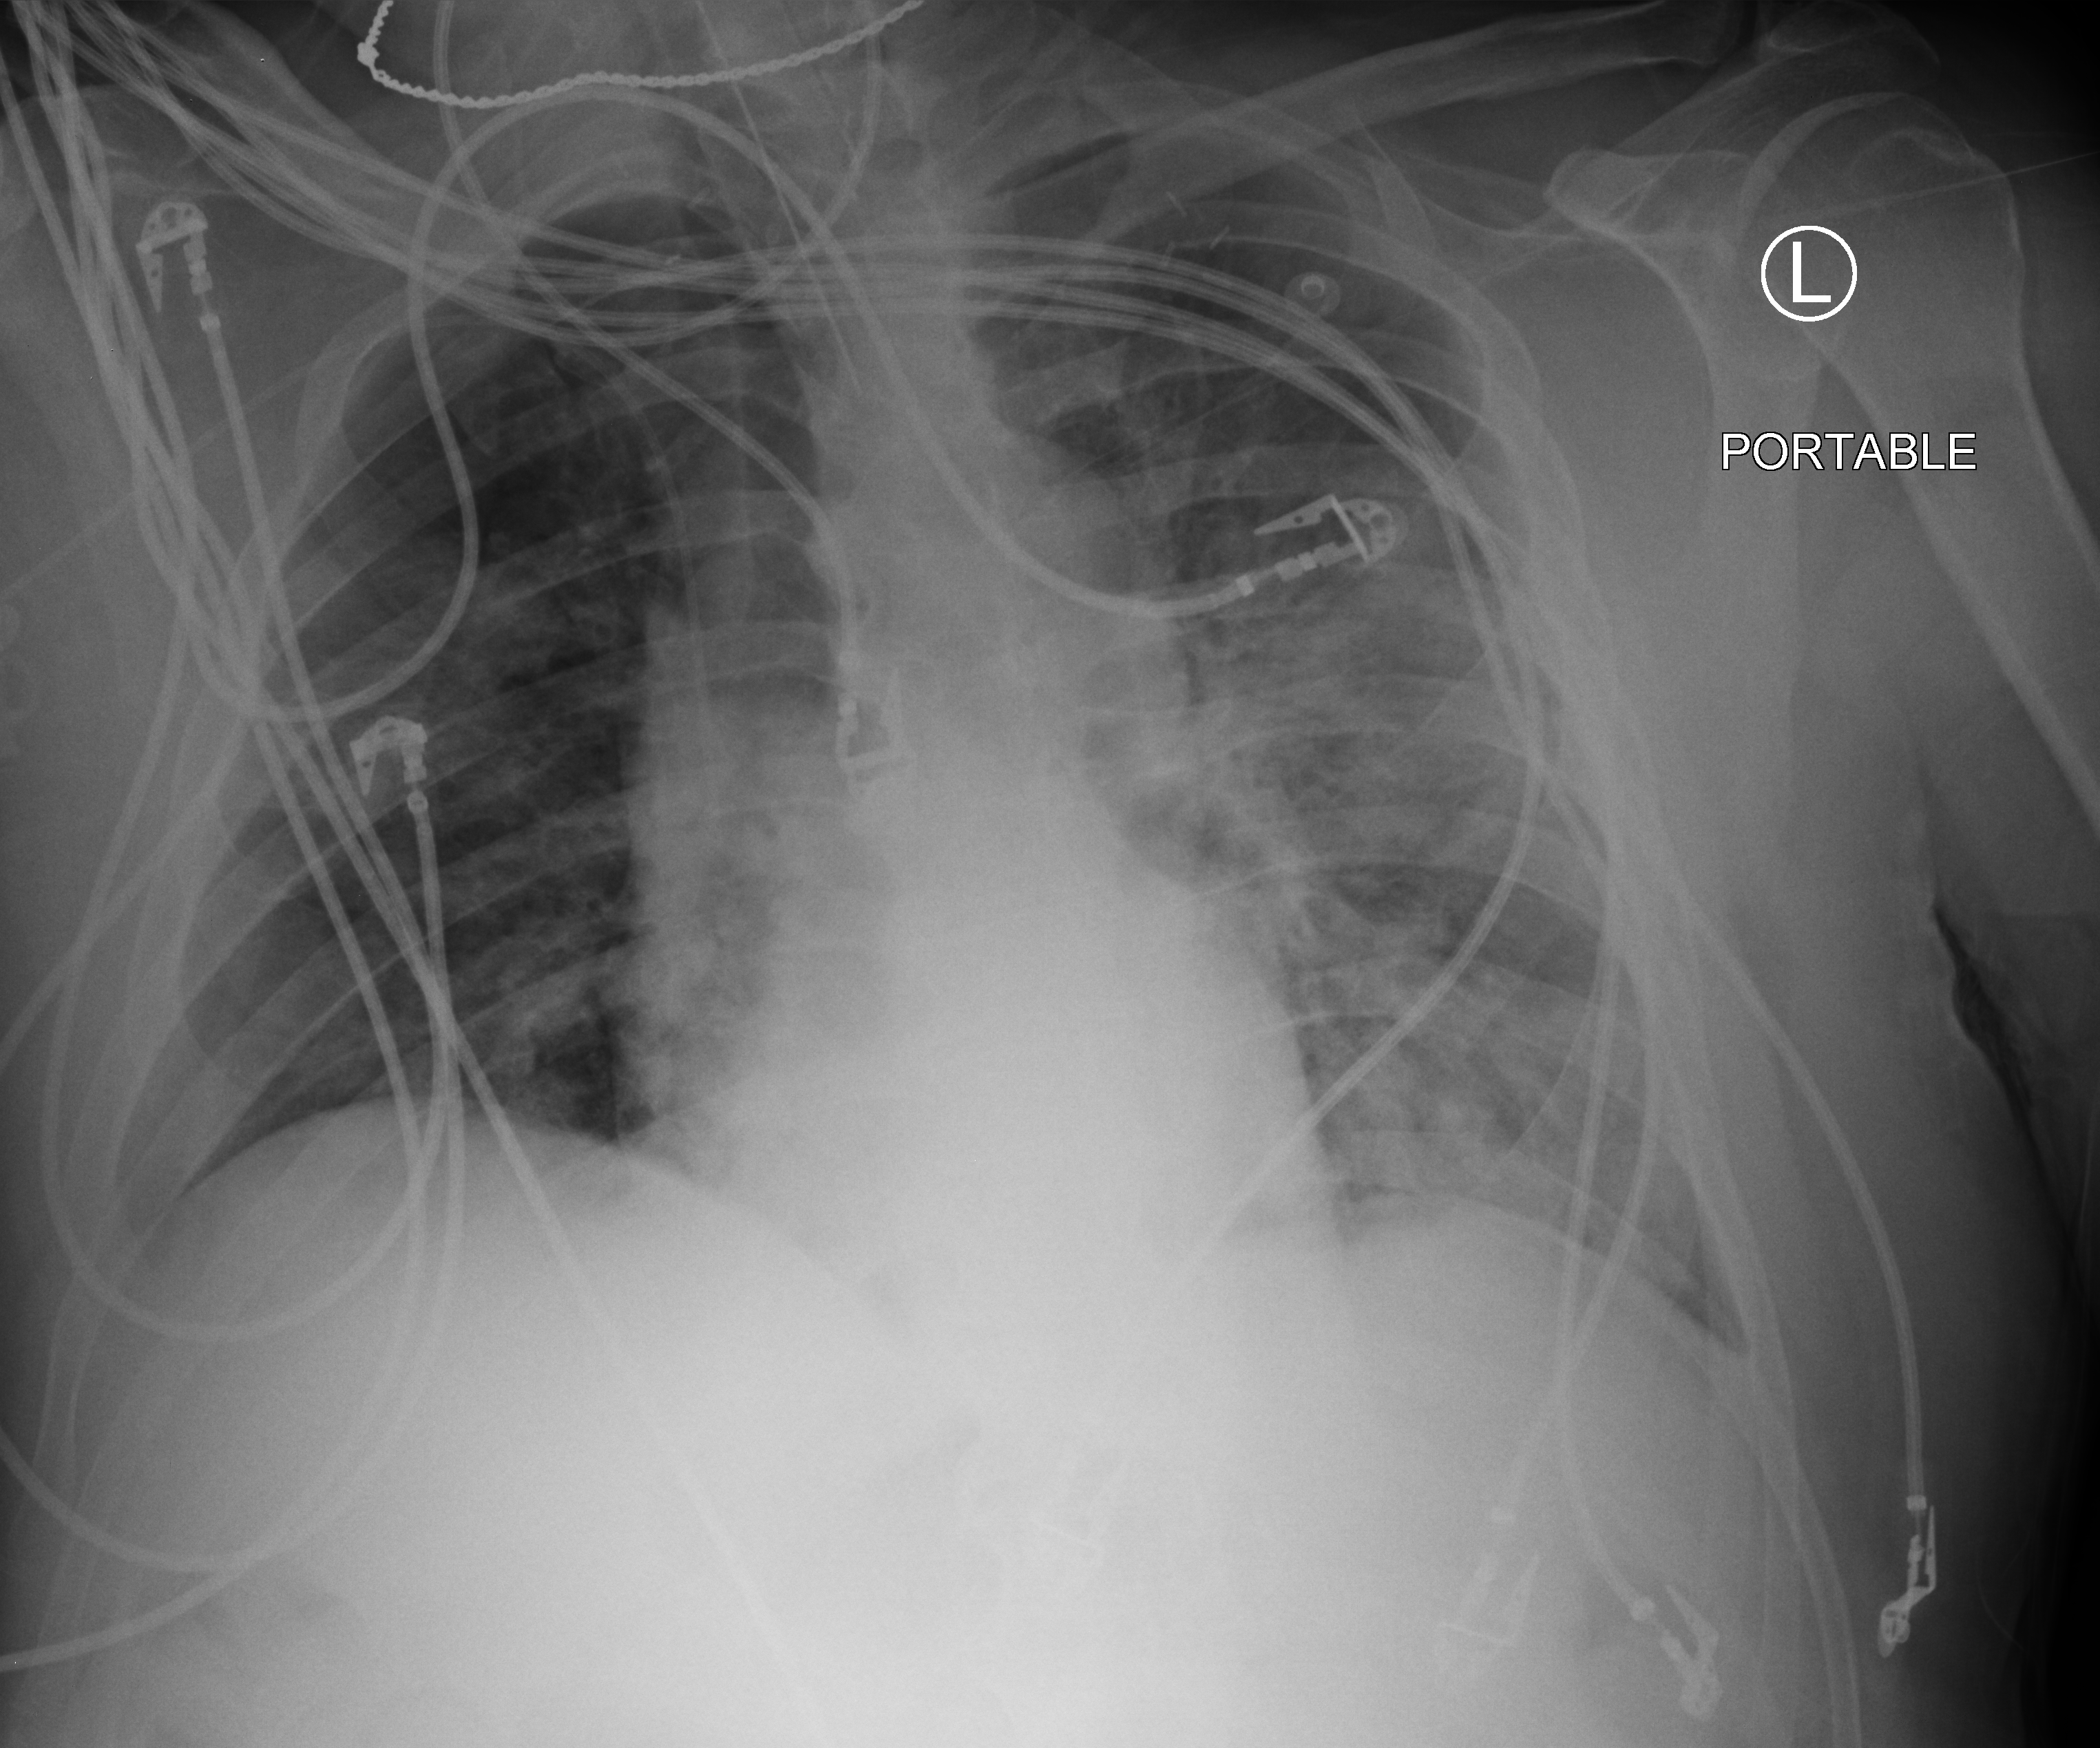
Portable chest radiograph, anteroposterior (AP) projection. Patient hospitalised with COVID-19, aged 18–59 years.
From the hospital-stay record, not from the radiograph (when in the stay this image was taken is not recorded): smoking status (admission record): never.